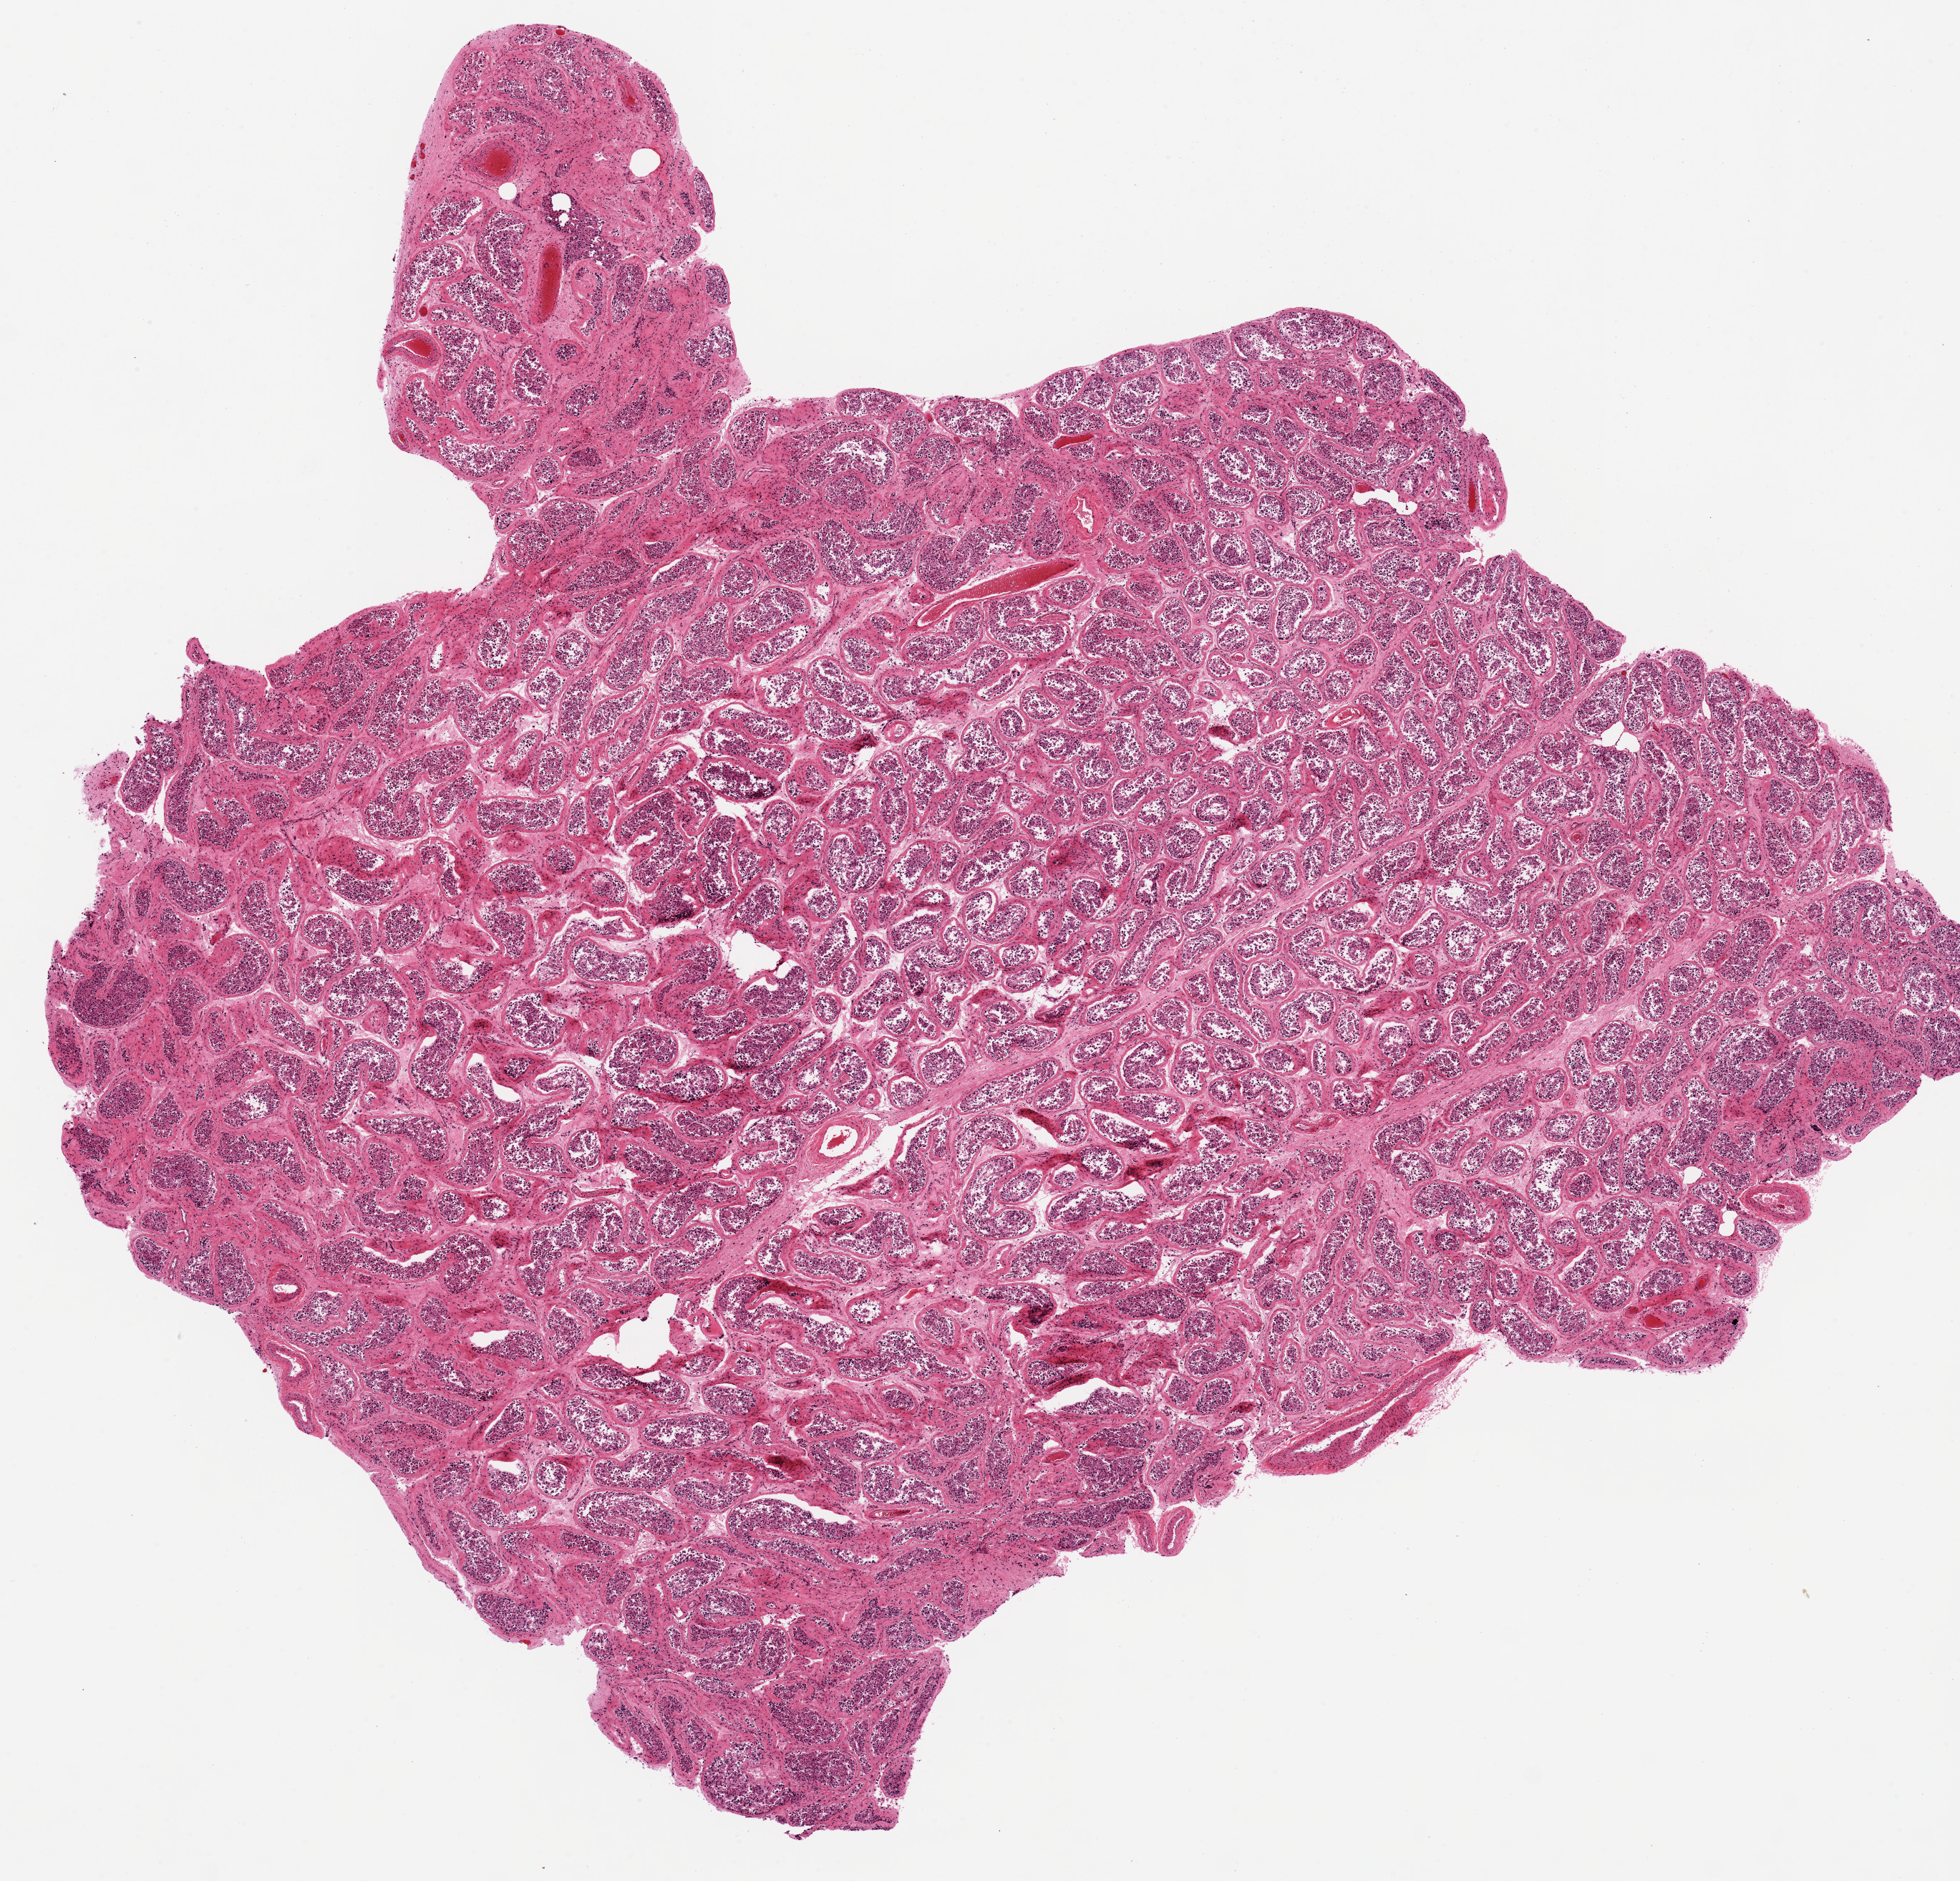
H&E whole-slide image, shown as a low-resolution overview of the whole scanned area (about 10.8 x 10.4 mm); PAXgene-fixed, paraffin-embedded tissue; section of testis (target tissue); donor tissue sample. Male donor.
• reviewer comment on this tissue sample: 1 piece 10x8 mm